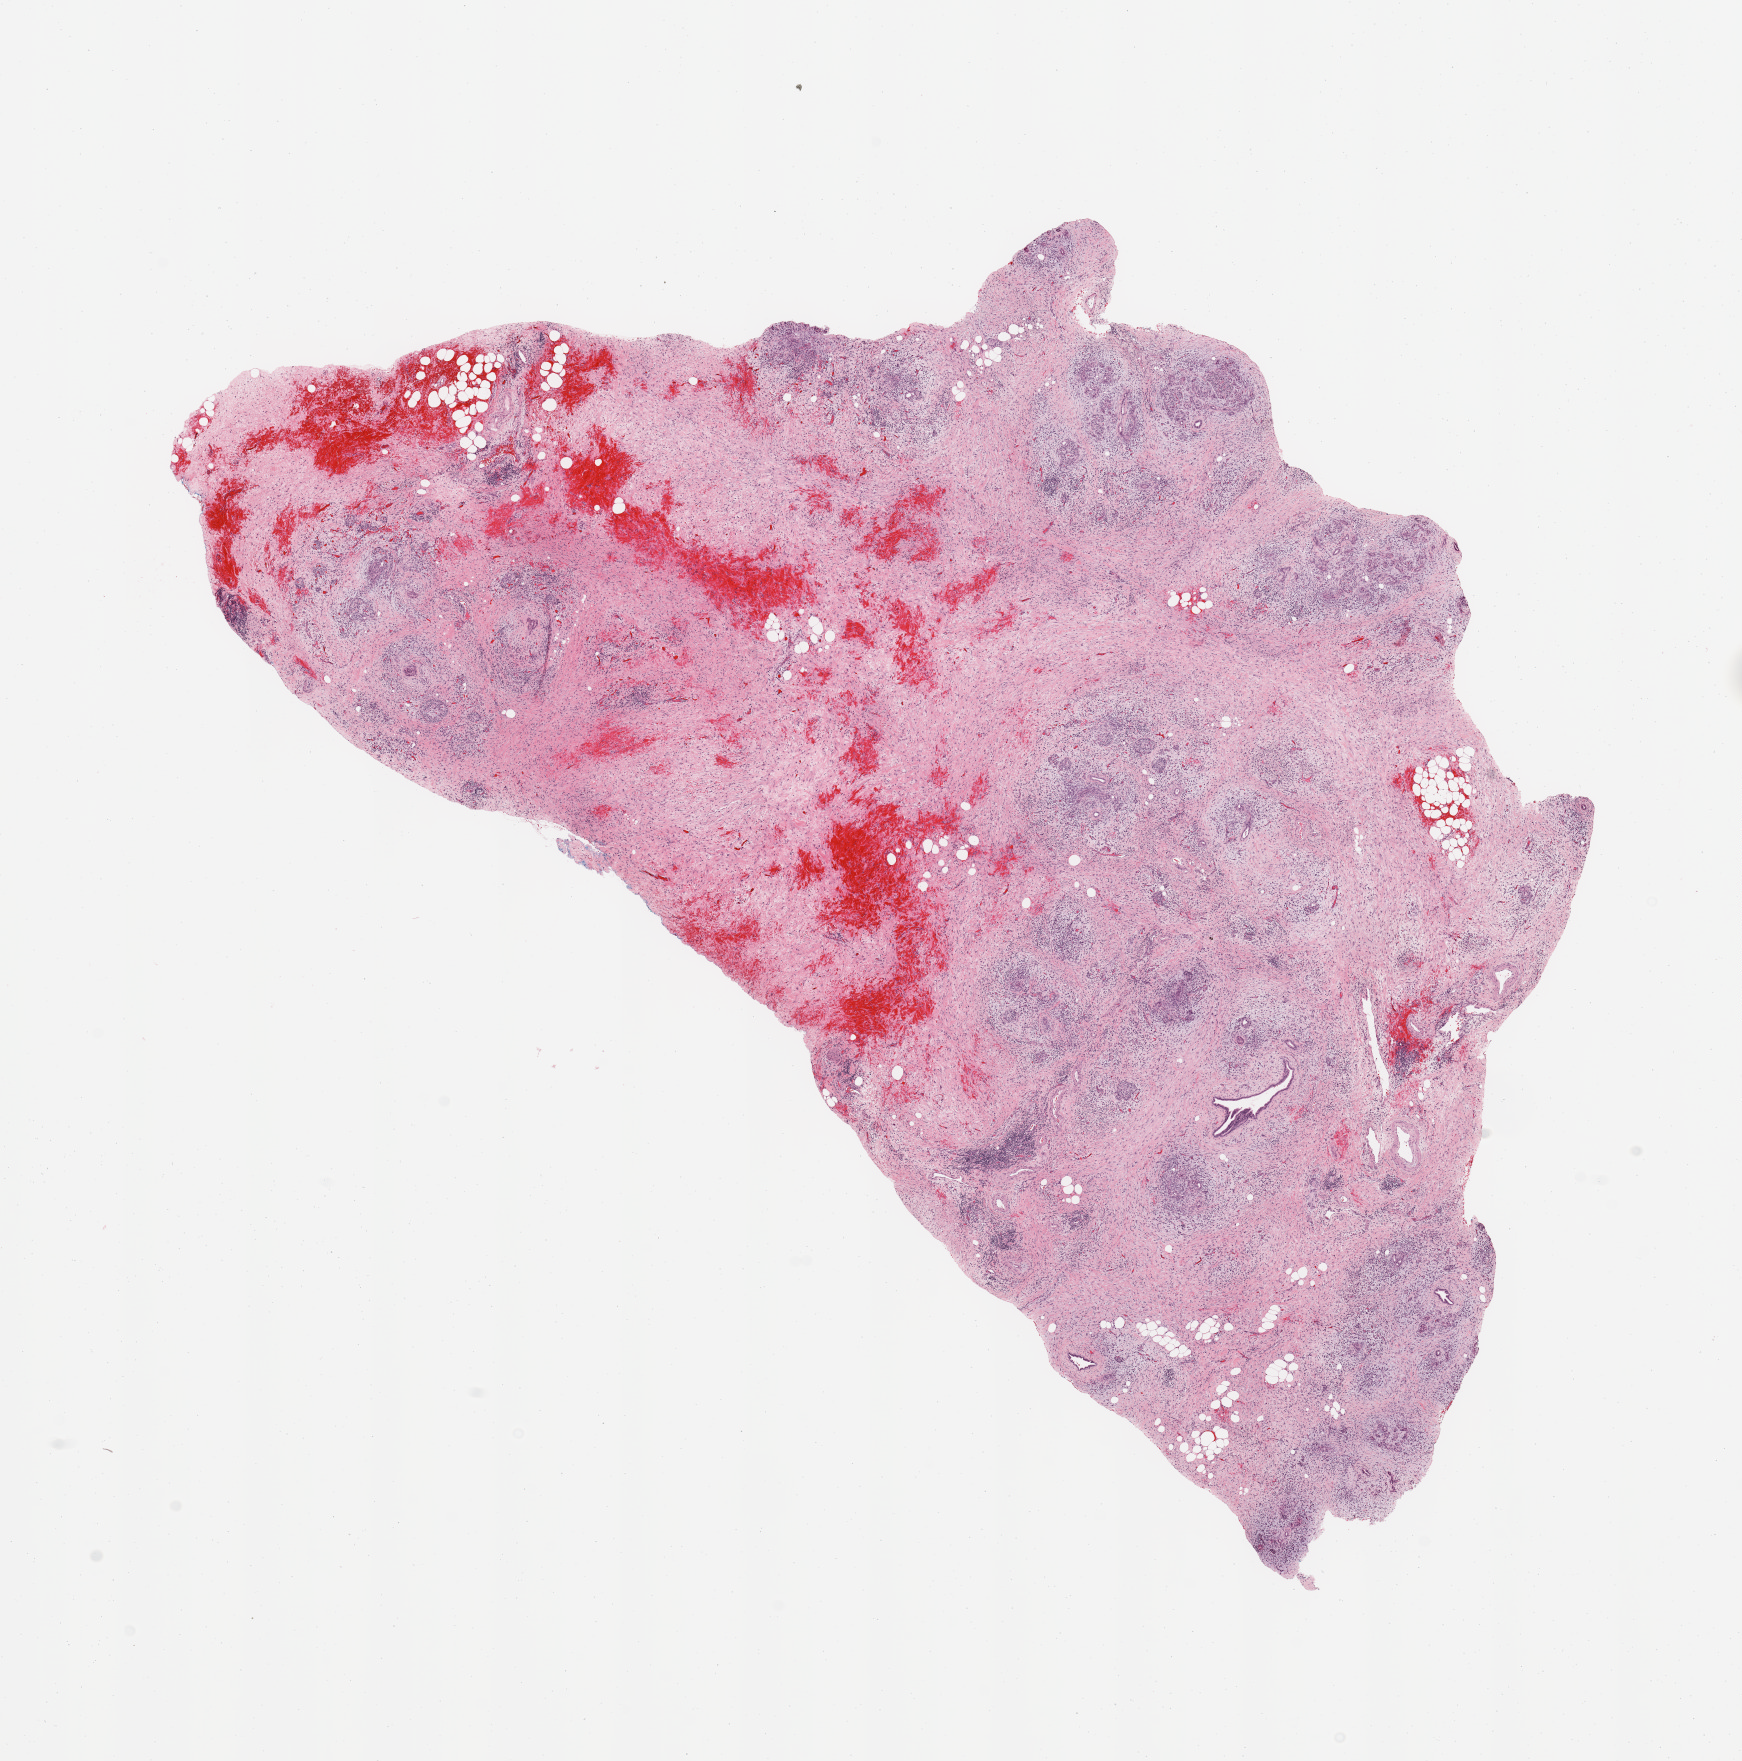
H&E-stained whole-slide image — whole scanned area (about 13.8 x 13.9 mm) shown as a low-resolution overview; normal (non-tumour) tissue sample, sampled site: pancreas. Male, 73 y/o.
- this section: normal (non-tumour) tissue from the same patient
- patient diagnosis: Infiltrating duct carcinoma, NOS